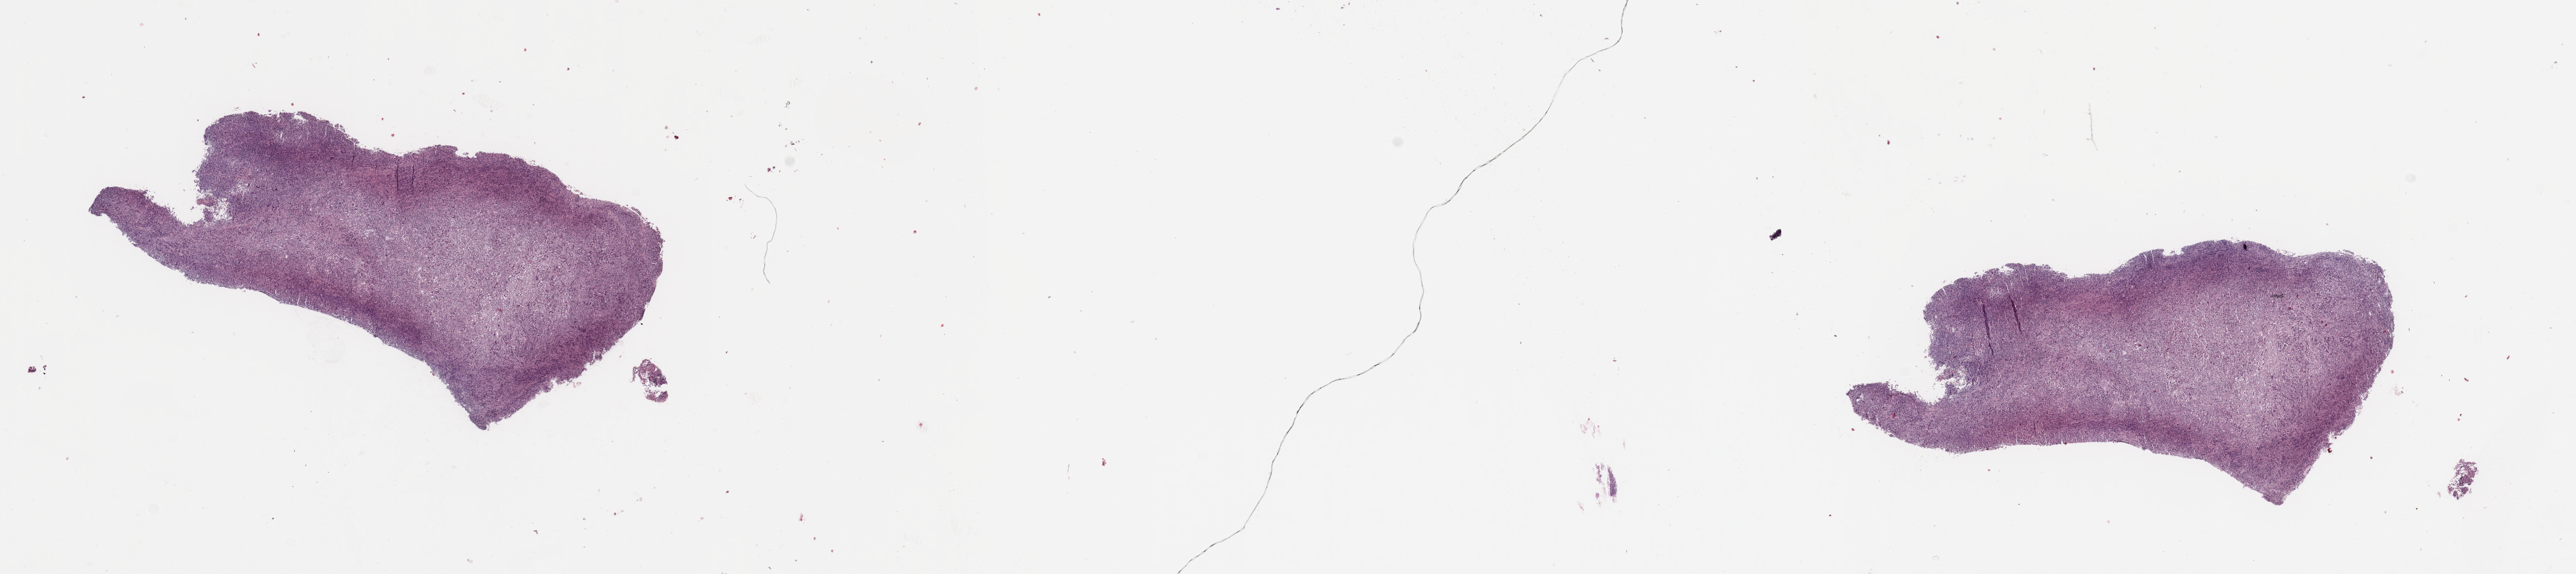
Whole-slide histology image, H&E, whole scanned area (about 28.5 x 6.4 mm, from a 20x scan) shown as a low-resolution overview. Tumour tissue sample, sampled site: lung. 64-year-old male patient. Histologic grade: G3 (poorly differentiated). Slide review estimates, as recorded: tumour nuclei 90%, necrosis 3%.
- AJCC pathologic stage: IA1
- histologic diagnosis: Adenocarcinoma, NOS